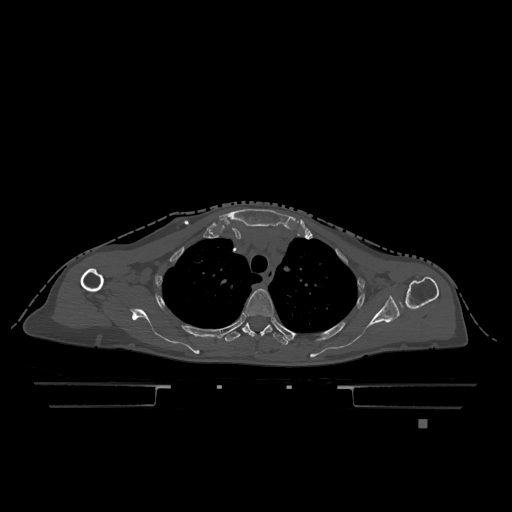
CT including the spine, one axial slice; position 904 of 1317 along the scan axis; bone window (W 1800 / L 400 HU); 0.5 mm slice thickness; 512 × 512 image matrix, field of view 500 × 500 mm. Patient: female, 74 years. From the clinical record (not read from this slice): primary cancer: lung; vertebrae with lytic lesions (as recorded): T1, T4, T5, T6, L4, L5.
Structures marked on this image (semi-automatic segmentation, software-assisted and operator-edited):
- T3 vertebra: bounding box (x1, y1, x2, y2) in pixels: (245, 289, 274, 317)
- T4 vertebra: (225, 322, 294, 345)